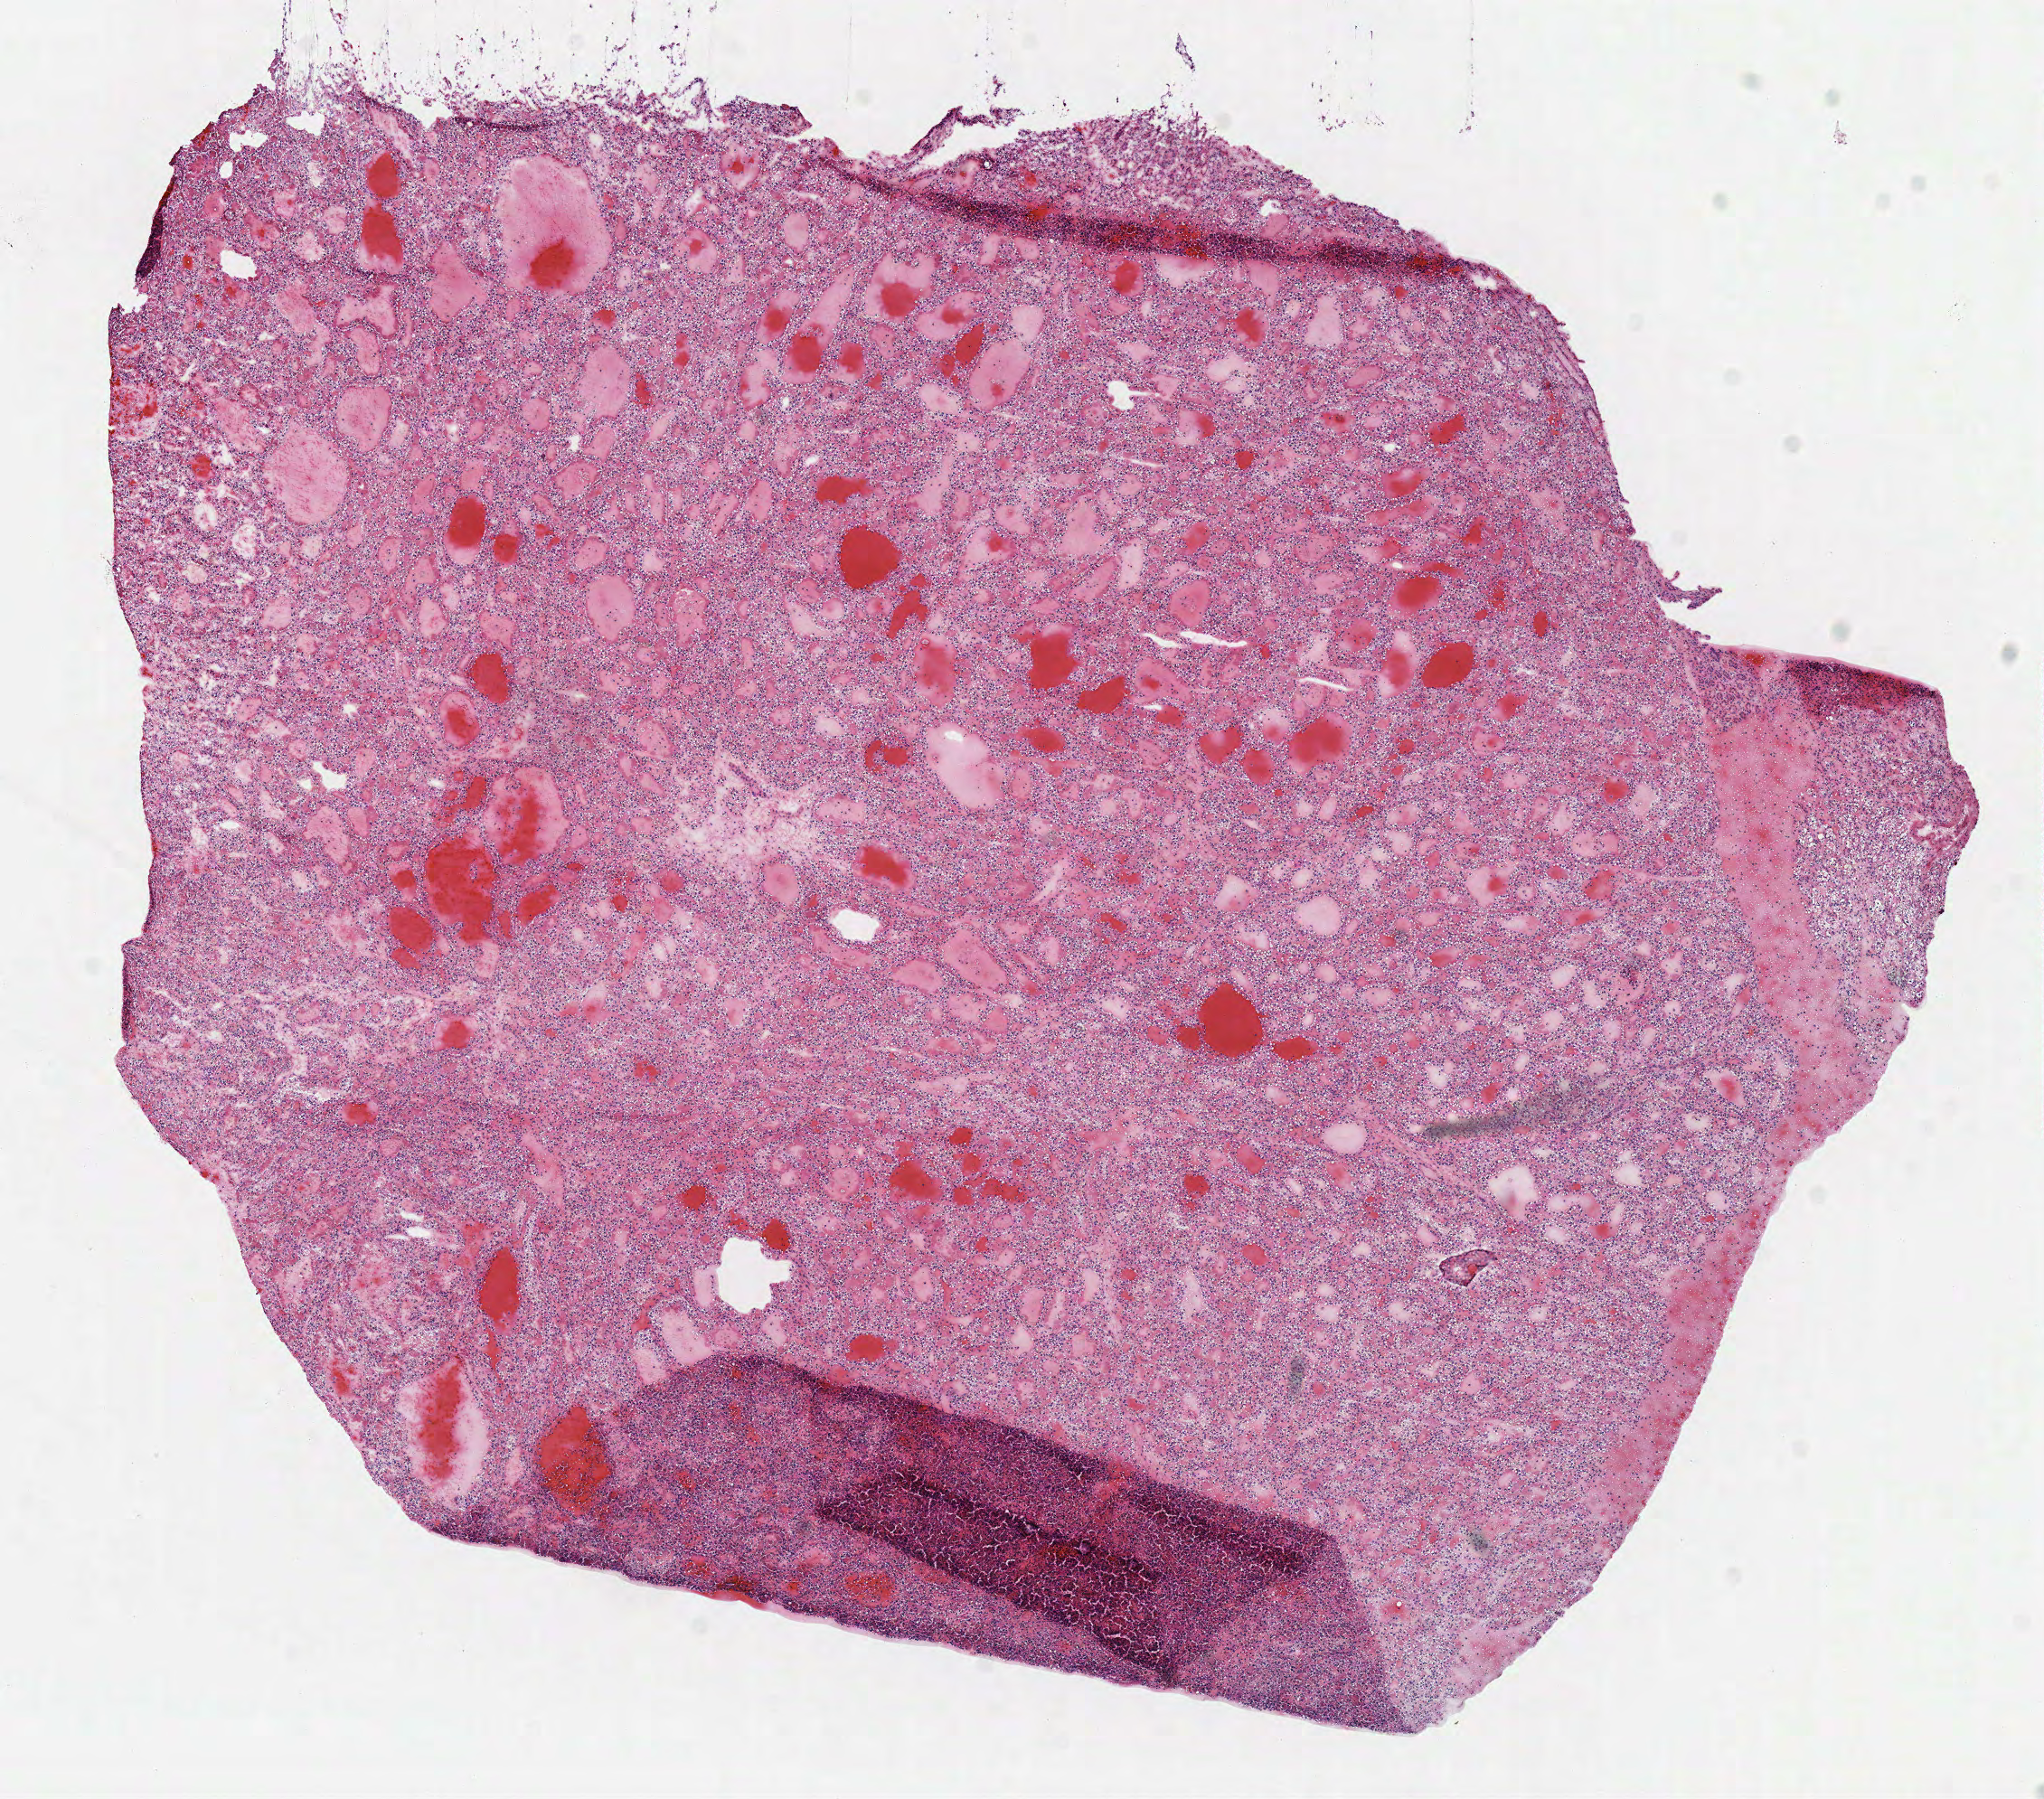
Digitized H&E tissue section (whole slide) — low-resolution overview of the scanned area, about 8.9 x 7.8 mm (slide scanned at 40x); frozen section from the top of the tissue portion; kidney, primary tumour sample. Female patient; age at initial diagnosis 44 years. Histologic grade: G2 (moderately differentiated). Composition of this section per pathologist review: tumour cells 95%, tumour nuclei 85%, normal cells 0%, stromal cells 5%, necrosis 0%.
AJCC pathologic stage: I. Laterality: right. Histologic diagnosis: Clear cell adenocarcinoma, NOS. TNM: T1a NX M0.